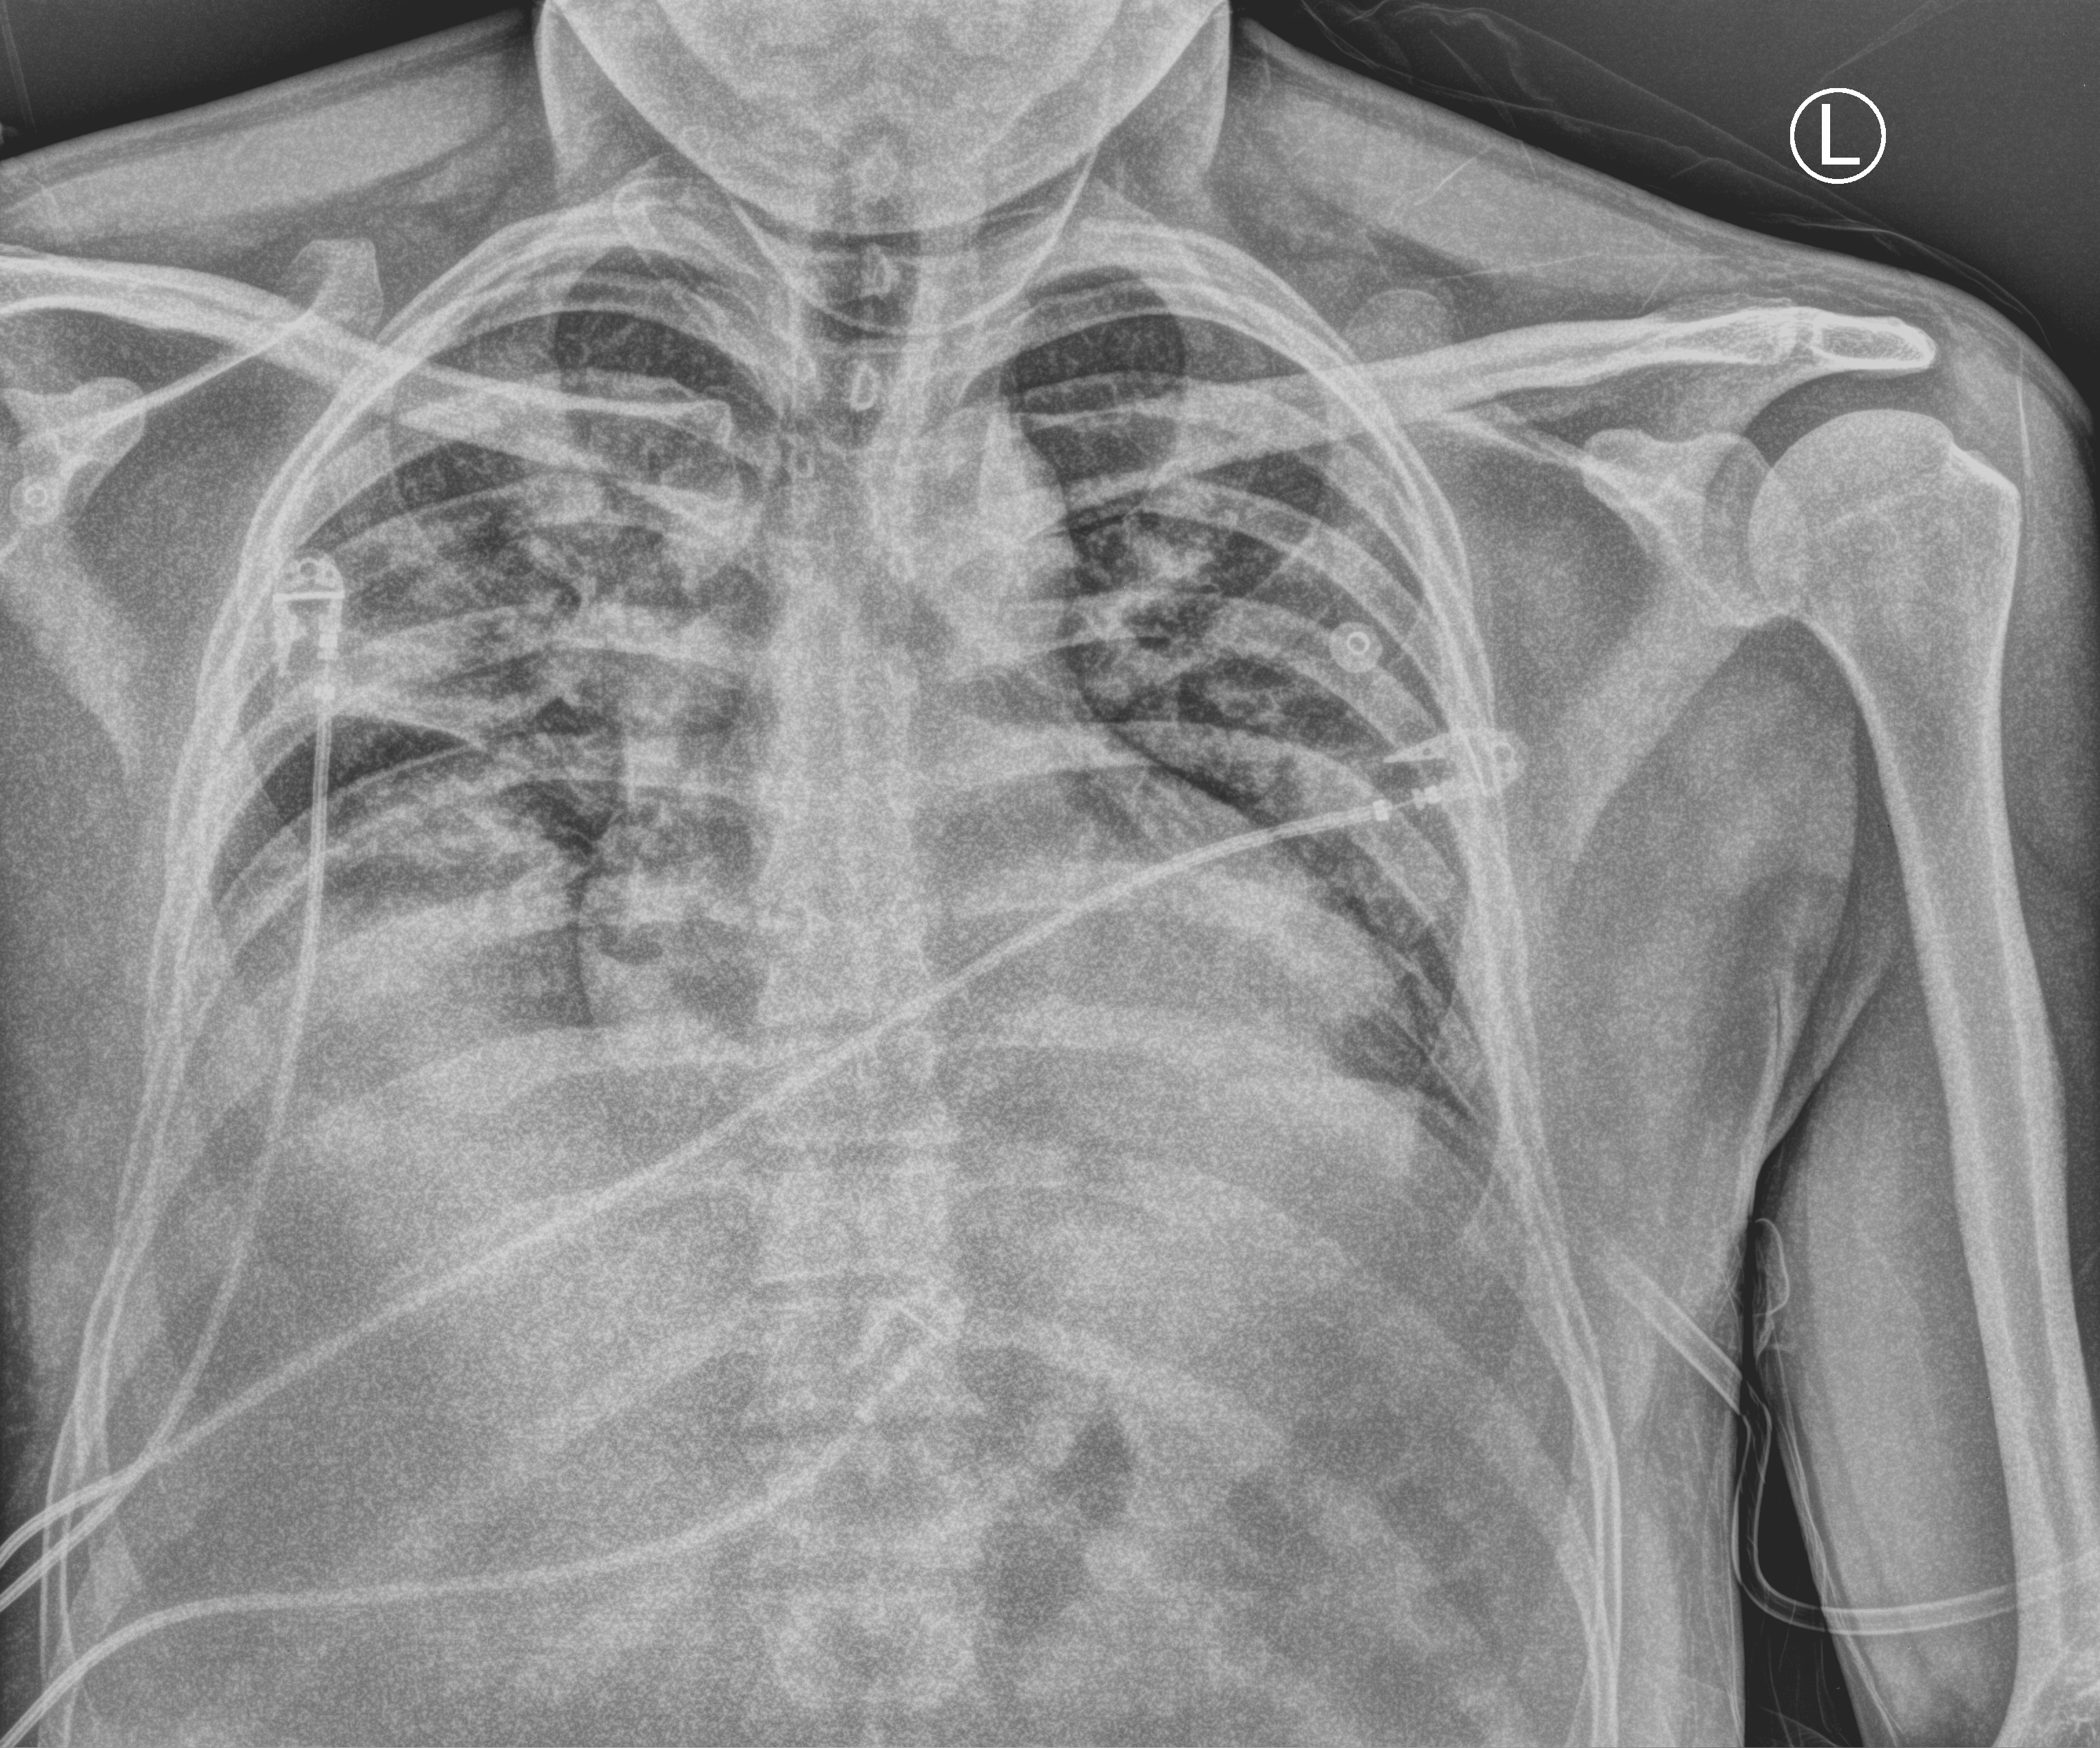
Chest X-ray (portable); anteroposterior (AP) projection. Patient hospitalised with COVID-19; male, aged 18–59 years.
Hospital-stay facts (about this admission, not read from this image; timing relative to this image not recorded): length of hospital stay: 15 days; admitted to intensive care during this hospital stay: no; mechanically ventilated during this hospital stay: no.